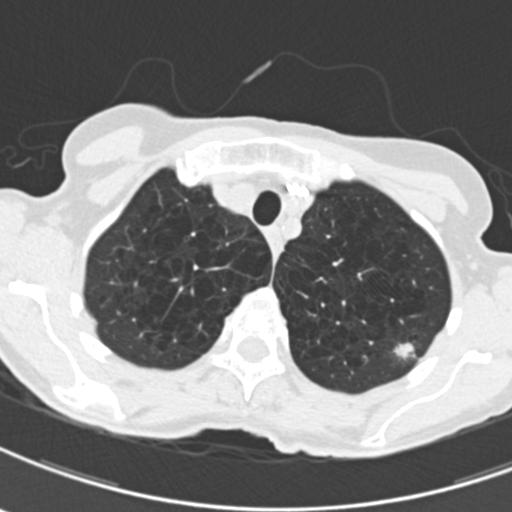
Low-dose screening chest CT, one axial slice; position 166 of 203 along the scan axis; 120 kVp; lung window (W 1500 / L -600 HU); 512 × 512 image matrix, field of view 279 × 279 mm.
Structures marked on this image (manually delineated by an expert):
- lesion 1 (tumor, upper lobe of left lung): bounding box [x1, y1, x2, y2] px = [393, 341, 416, 358]